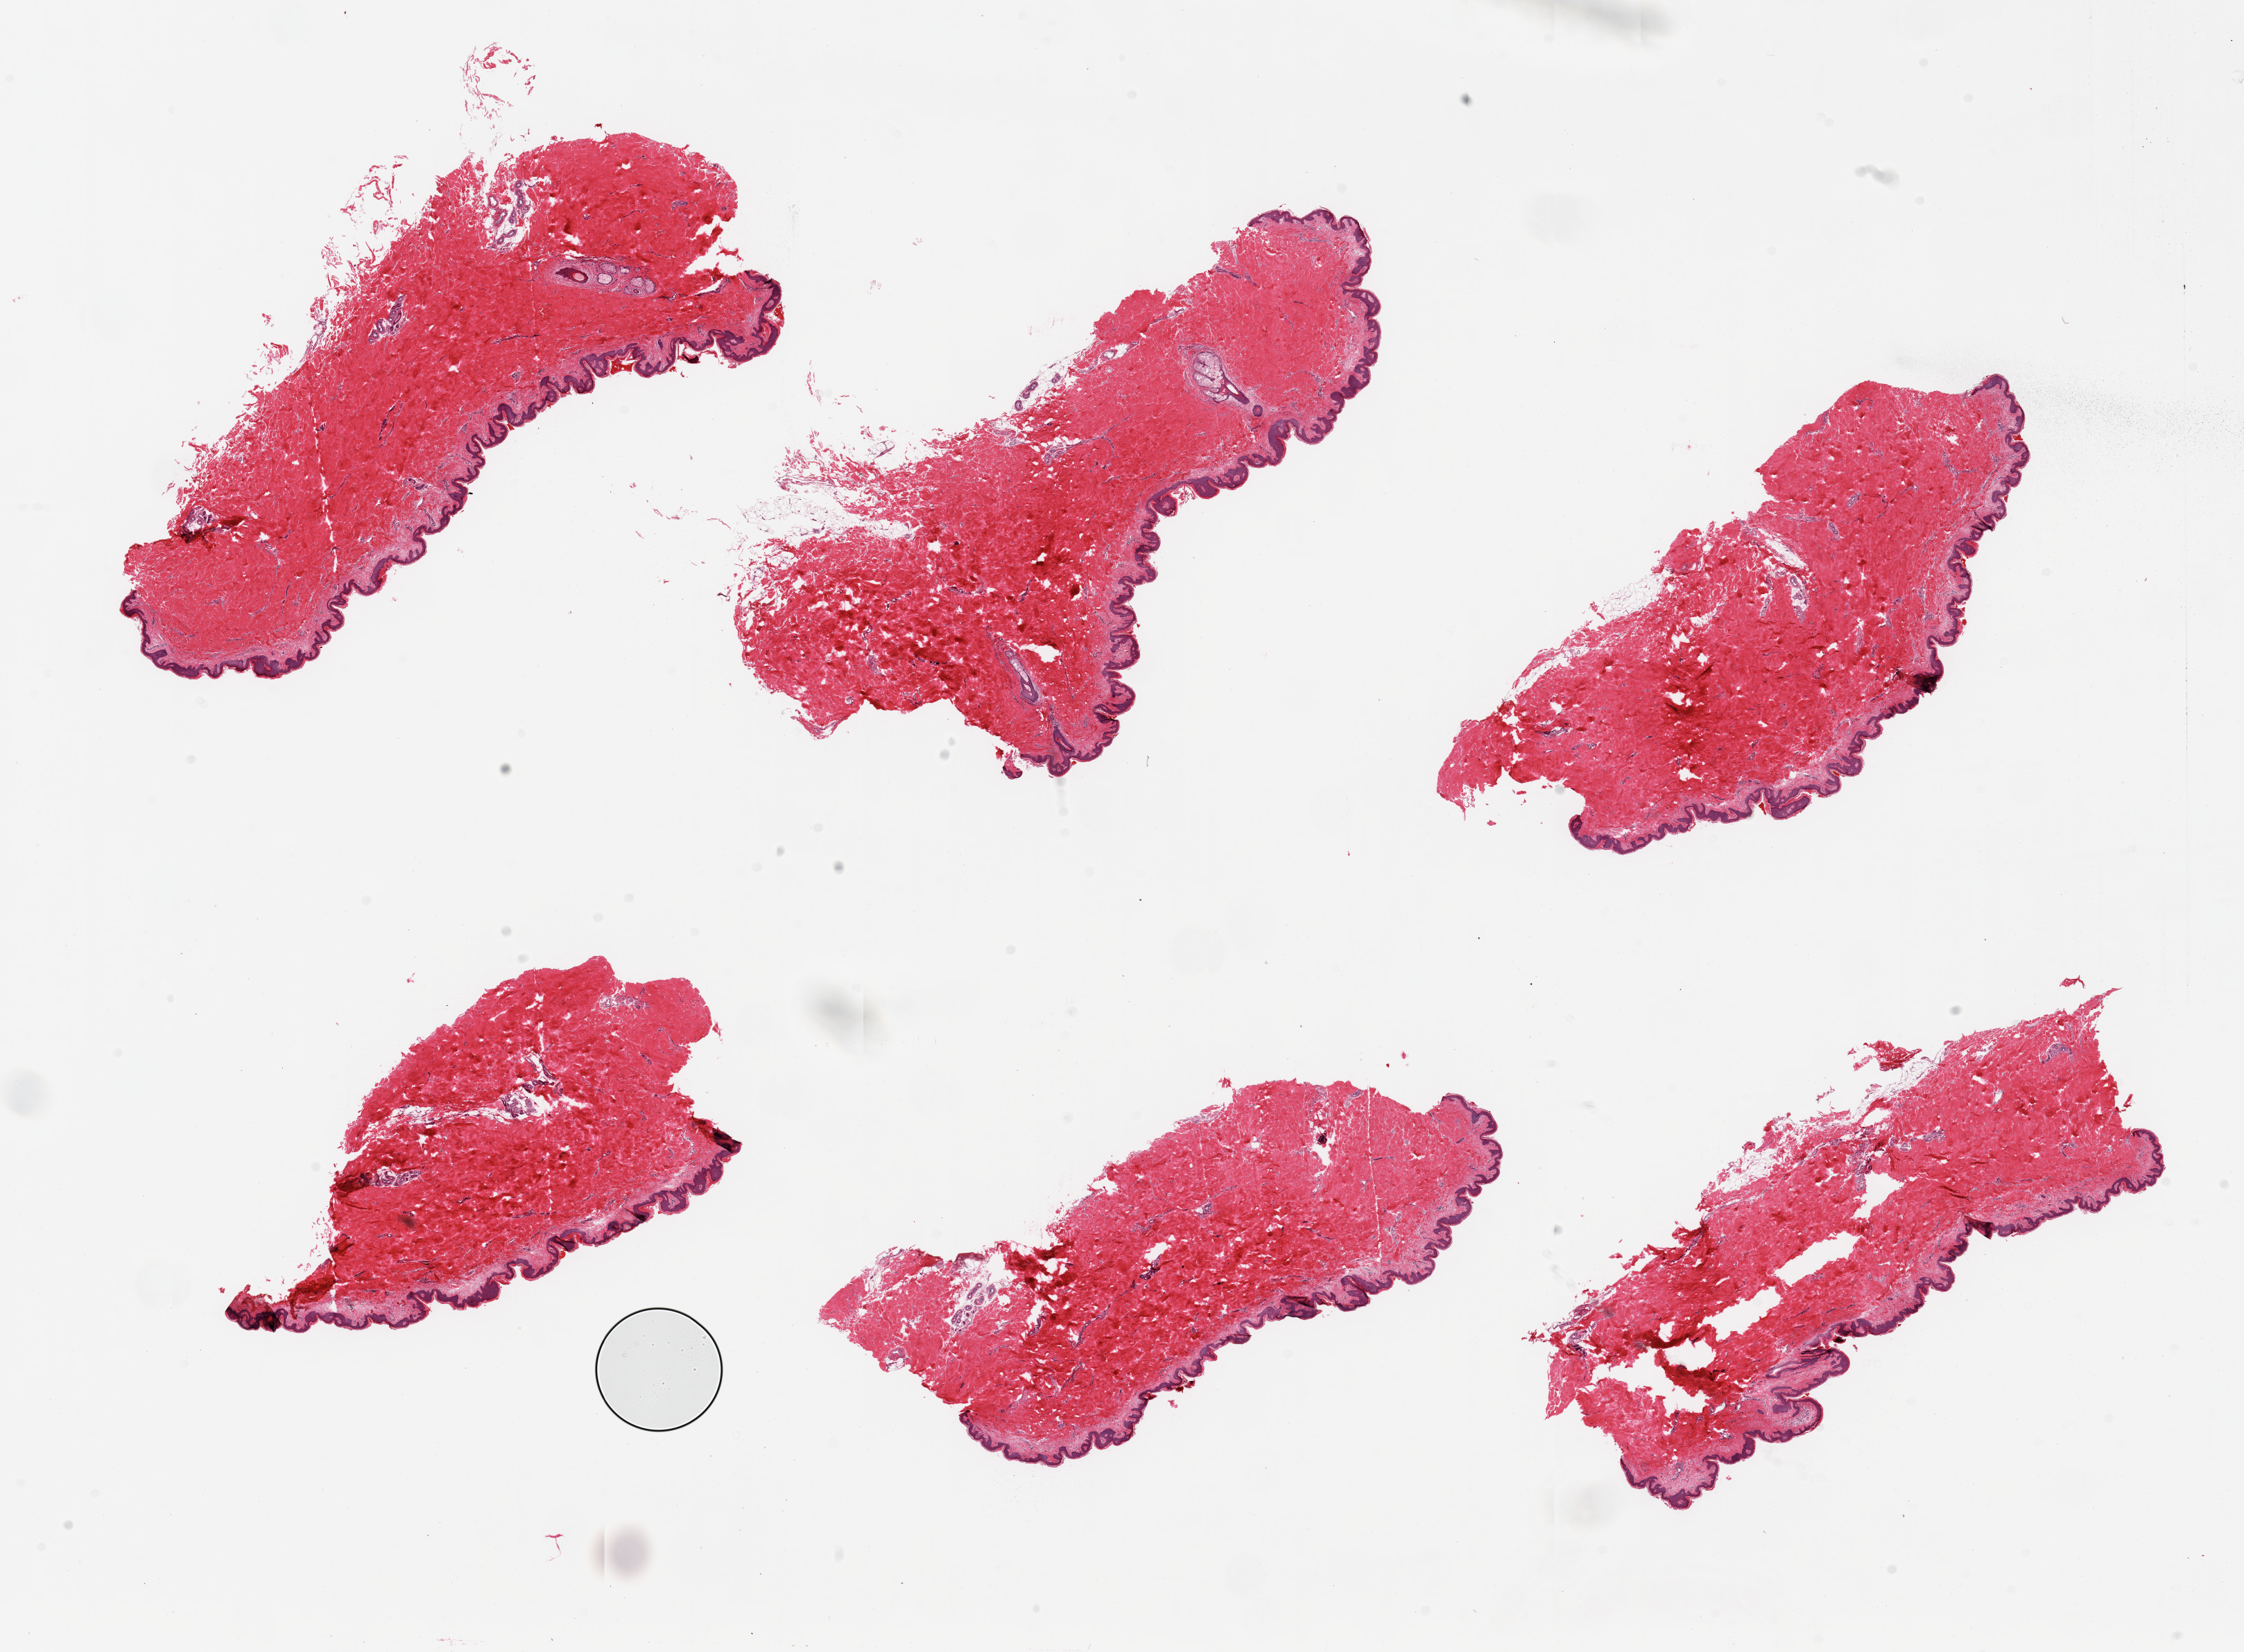
Digitized hematoxylin and eosin (H&E)-stained section — a low-resolution overview of the entire scanned area, about 25.6 x 18.8 mm (from a 20x scan); PAXgene-fixed, paraffin-embedded tissue; section of skin of suprapubic region (target tissue); donor tissue sample.
Review note (as recorded): 6 pieces, no dermal fat; squamous epithelium is ~50 microns.